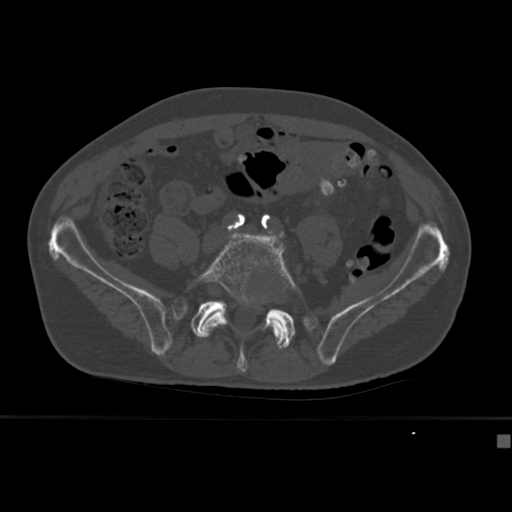
CT including the spine, one axial slice; slice 82 of 430 in the series (ordered by position); bone window (W 1800 / L 400 HU); 1.5 mm slice thickness; 512 × 512 image matrix. Male patient, age 64 years. Case-level facts recorded for this patient, not image findings: primary cancer: uterus; vertebrae with lytic lesions (as recorded): T1, T4, T5, T7, L5.
Annotated regions visible in this slice (semi-automatic segmentation, software-assisted and operator-edited):
- L5 vertebra: bounding box <196,233,299,349> (left, top, right, bottom; pixels)